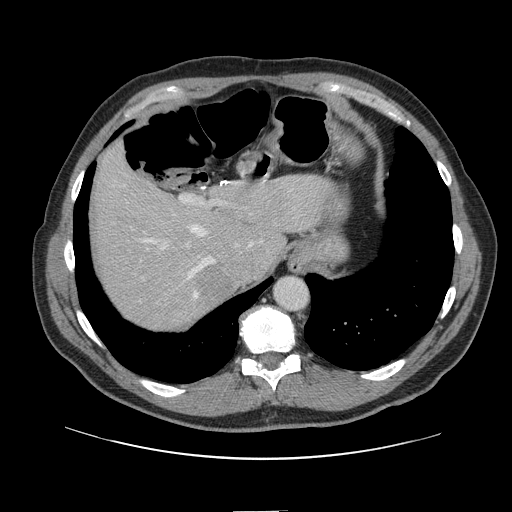
Contrast-enhanced abdominal CT, one axial slice; position 112 of 161 along the scan axis; 120 kVp; soft-tissue window (W 400 / L 40 HU); 512 × 512 image matrix, field of view 412 × 412 mm. Male patient, age 66 years. Case-level facts recorded for this patient, not image findings: diagnosis: colorectal cancer liver metastases, imaged before liver resection; multiple liver metastases: no; largest metastasis: 3.5 cm; disease in both lobes: no.
Outlined on this slice (manually delineated by an expert):
- hepatic veins: bounding box (x1, y1, x2, y2) in pixels: (136, 225, 216, 300)
- liver: (94, 148, 325, 330)
- planned liver remnant (the part of the liver to remain after resection): (93, 149, 326, 305)
- portal vein (with intrahepatic branches): (180, 195, 228, 248)
- liver metastasis: (194, 264, 225, 305)